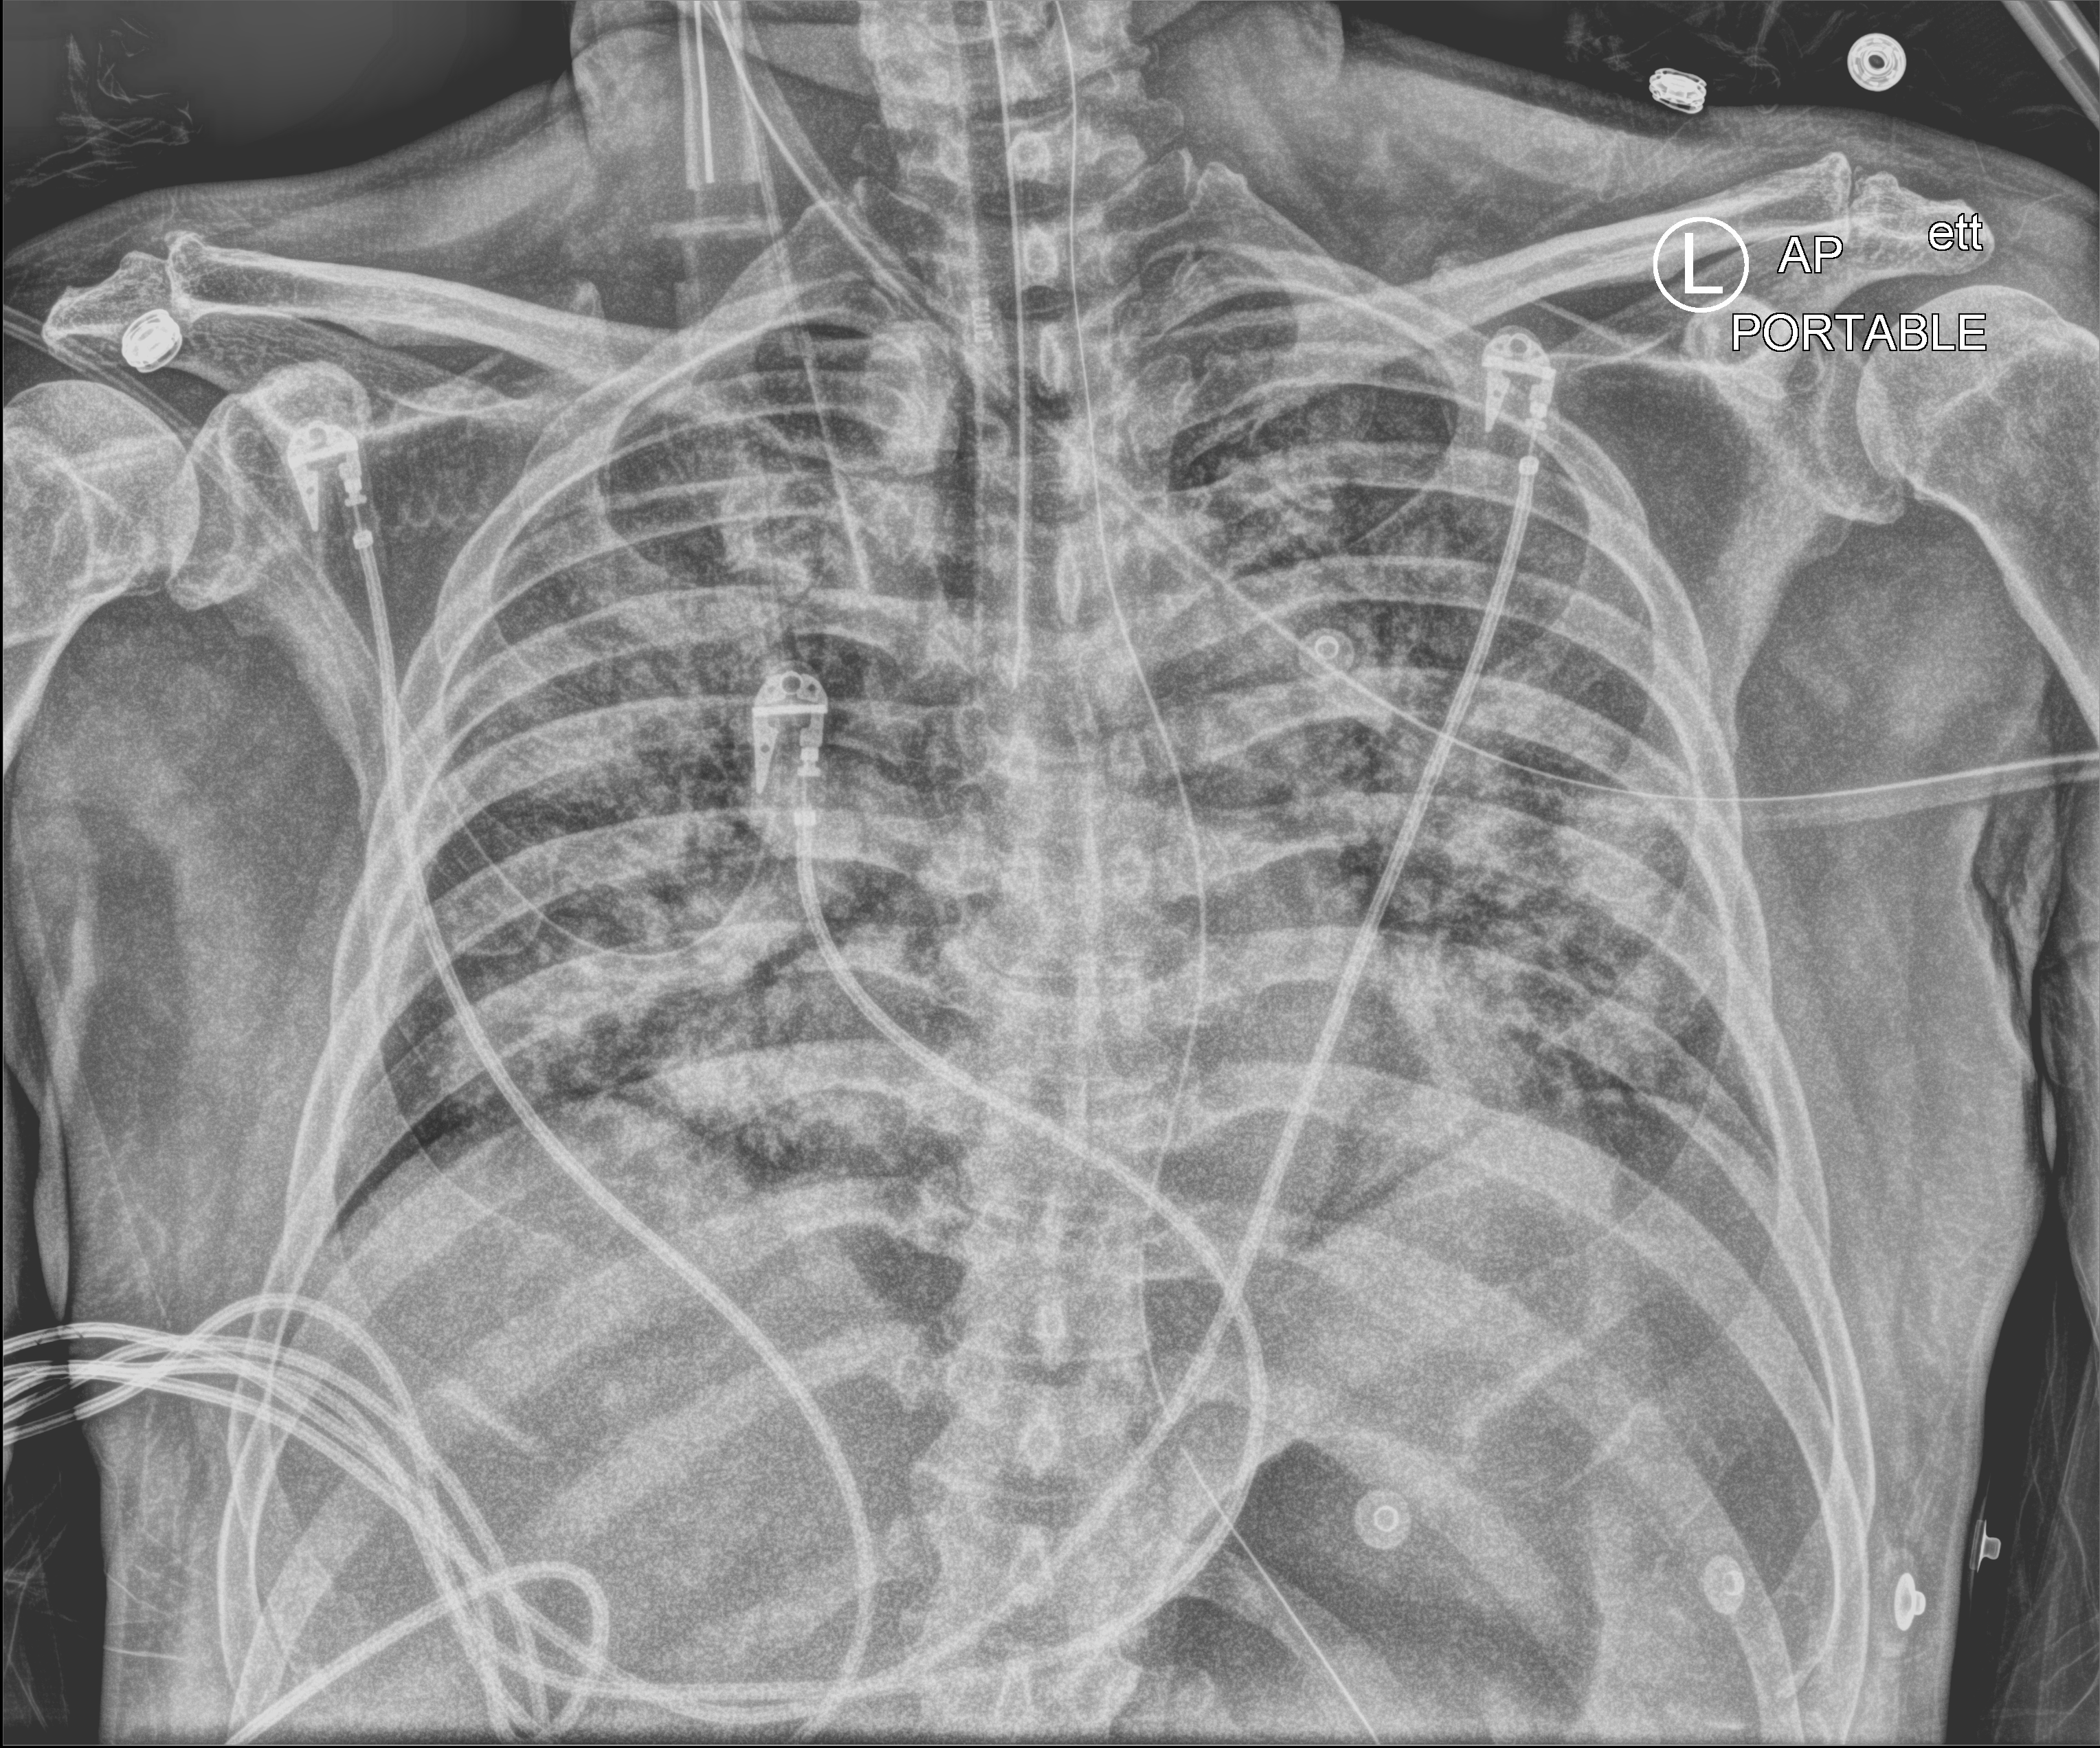
Chest X-ray (portable); anteroposterior (AP) projection. Male patient hospitalised with COVID-19, age 60–74 years.
Admission-level facts for this patient (not findings on this image; timing relative to this image not recorded):
- chronic kidney disease (admission record): no
- mechanically ventilated during this hospital stay: yes
- admitted to intensive care during this hospital stay: yes